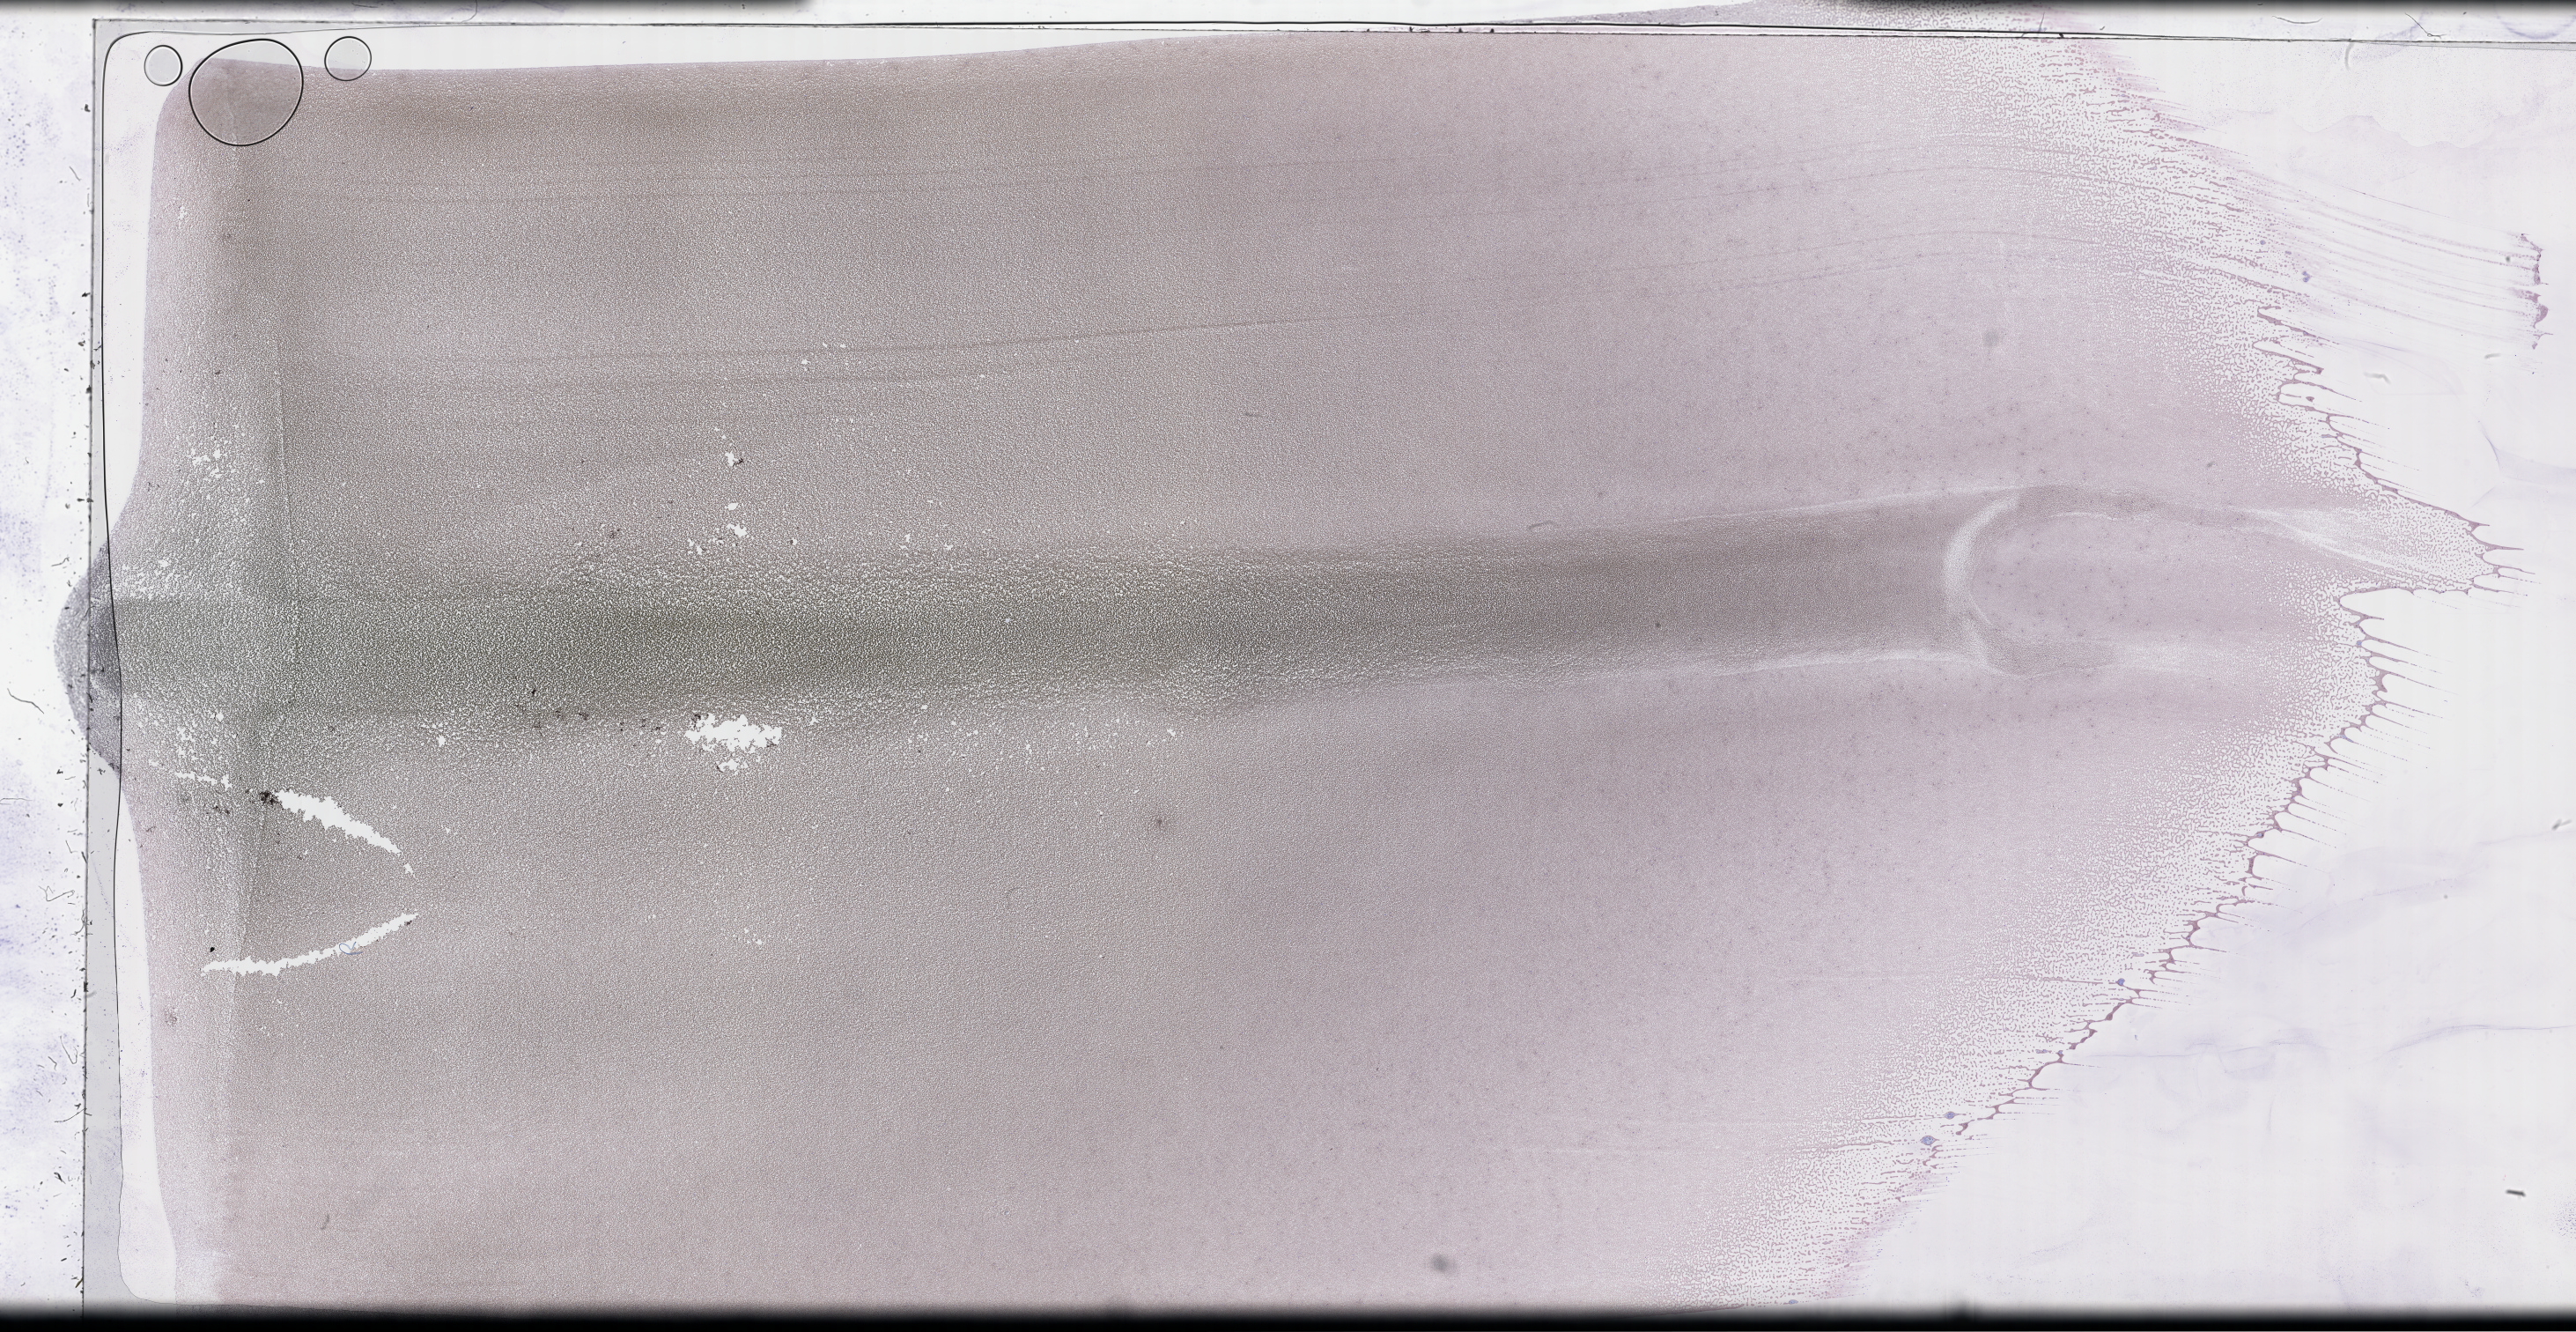
Wright-Giemsa-stained whole blood smear, whole-slide image, low-resolution overview of the scanned area, about 47.2 x 24.4 mm, smear from an EDTA sample, collected on treatment. Female patient.
Patient diagnosis: Plasma Cell Myeloma.